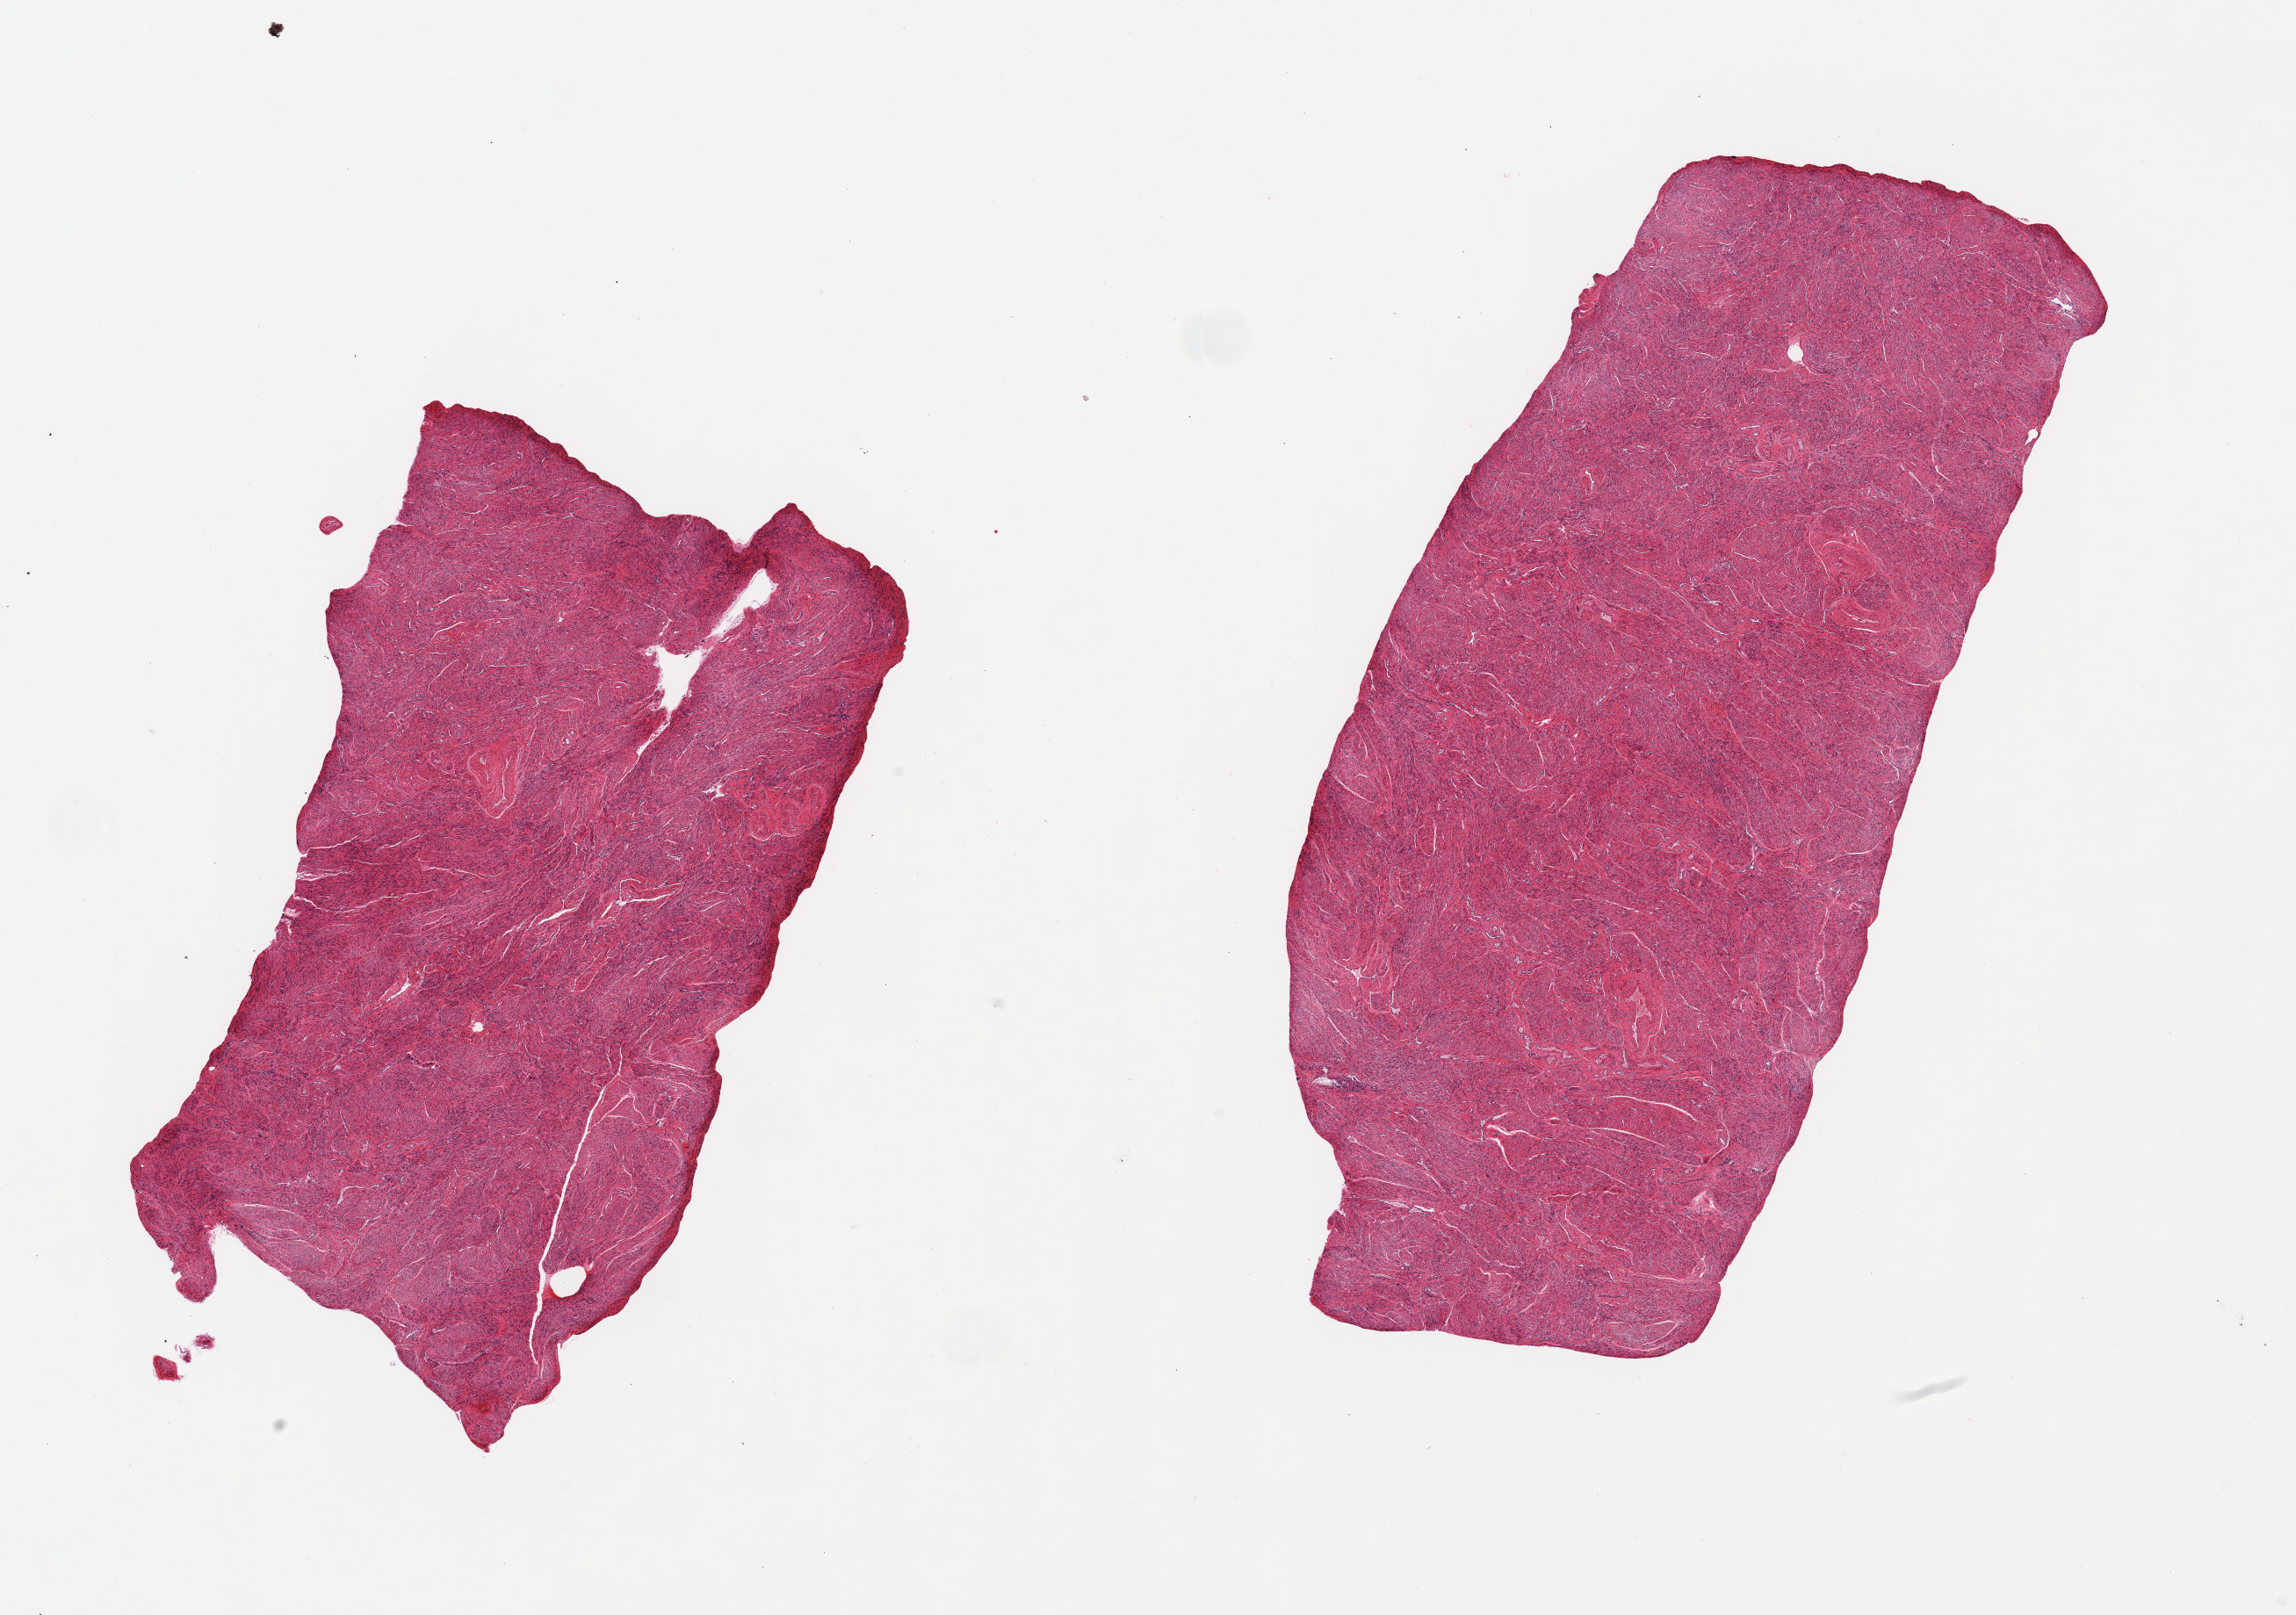
Whole-slide image, H&E stain, brightfield — a low-resolution overview of the entire scanned area, about 20.7 x 14.5 mm (slide scanned at 20x); PAXgene-fixed paraffin-embedded (PFPE) section; target tissue: uterus; tissue donor sample. Female donor.
Review note (as recorded): 2 pieces; myometrium only in this section.